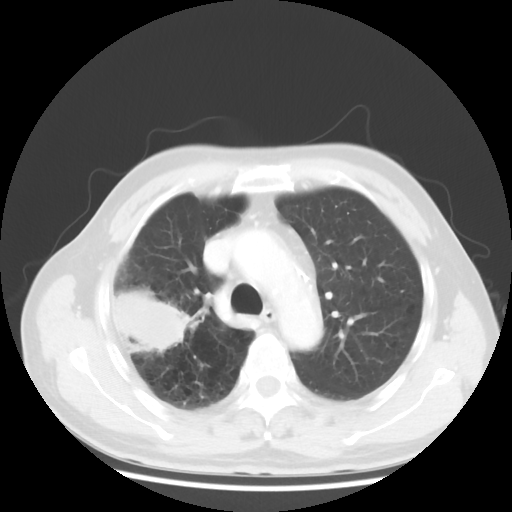
Chest CT, one axial slice. Slice 36 of 50 in the series (ordered by position). Reconstruction kernel STANDARD. Lung window (W 1500 / L -600 HU). 512 × 512 image matrix, field of view 360 × 360 mm. Patient: male, 69 years. From the clinical record (not read from this slice): clinical TNM (as recorded): T3 N0 M0; histopathological grade: G3.
Annotated regions visible in this slice (rectangle marked by the reading radiologist):
- lung tumour (recorded histology: adenocarcinoma): bounding box <112,279,196,361> (left, top, right, bottom; pixels)